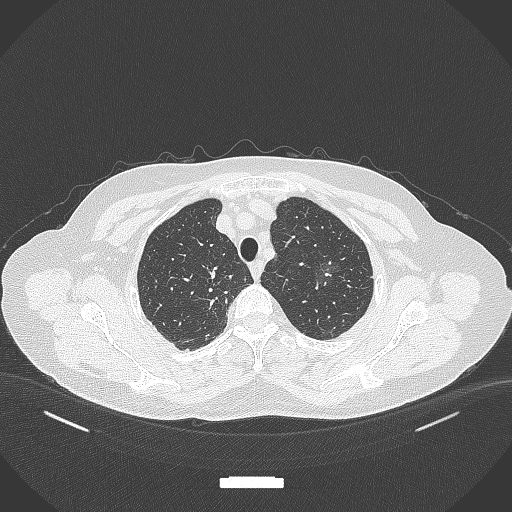
Chest CT, one axial slice; slice 298 of 369 in the series (ordered by position); reconstruction kernel B70f; lung window (W 1500 / L -600 HU); 1 mm slice thickness; 512 × 512 image matrix, field of view 400 × 400 mm. Female patient, age 64 years. From the clinical record (not read from this slice): clinical TNM (as recorded): T1c N0 M0; histopathological grade: G1.
Structures marked on this image (bounding box drawn by a radiologist):
- lung tumour (recorded histology: adenocarcinoma): bounding box <305,255,350,293> (left, top, right, bottom; pixels)